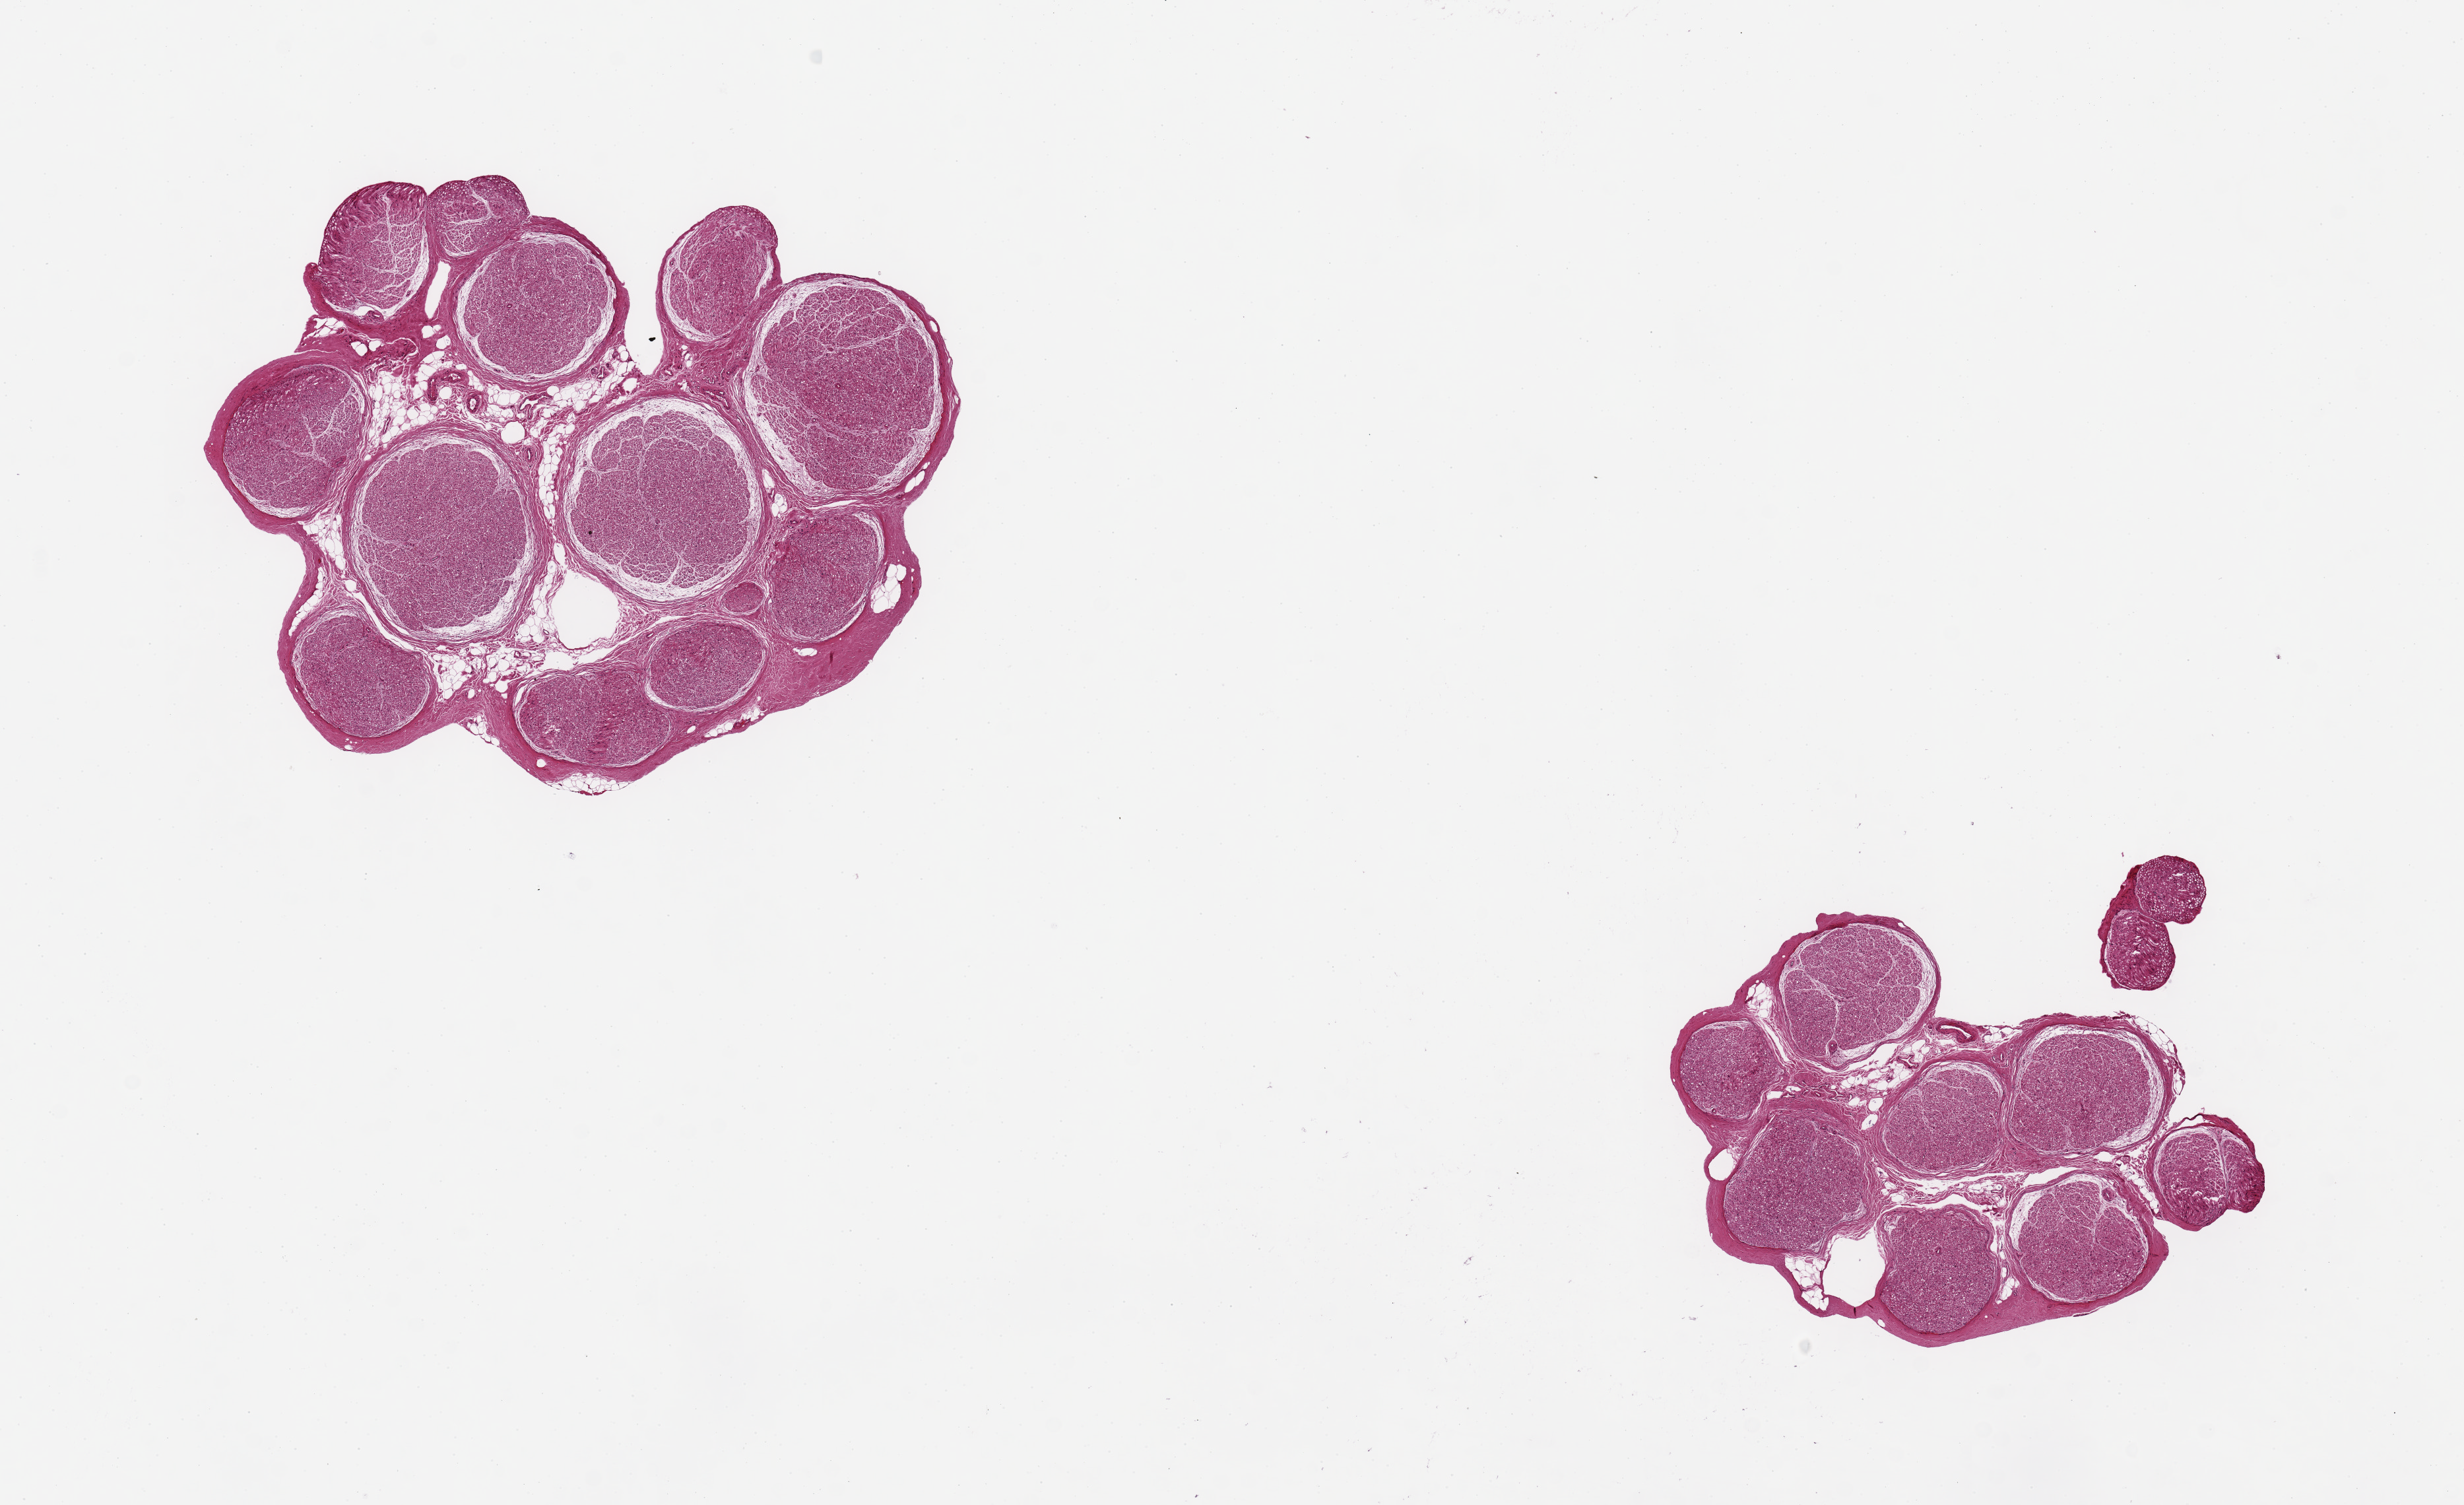
Digitized H&E-stained section, shown as a low-resolution overview of the whole scanned area (about 14.8 x 9.0 mm). PAXgene-fixed, paraffin-embedded tissue. Sampled site (target tissue): tibial nerve. Donor tissue sample.
Pathologist's review note for this sample: 2 pieces, ~3.5mm, good clean specimen, minimal fat.